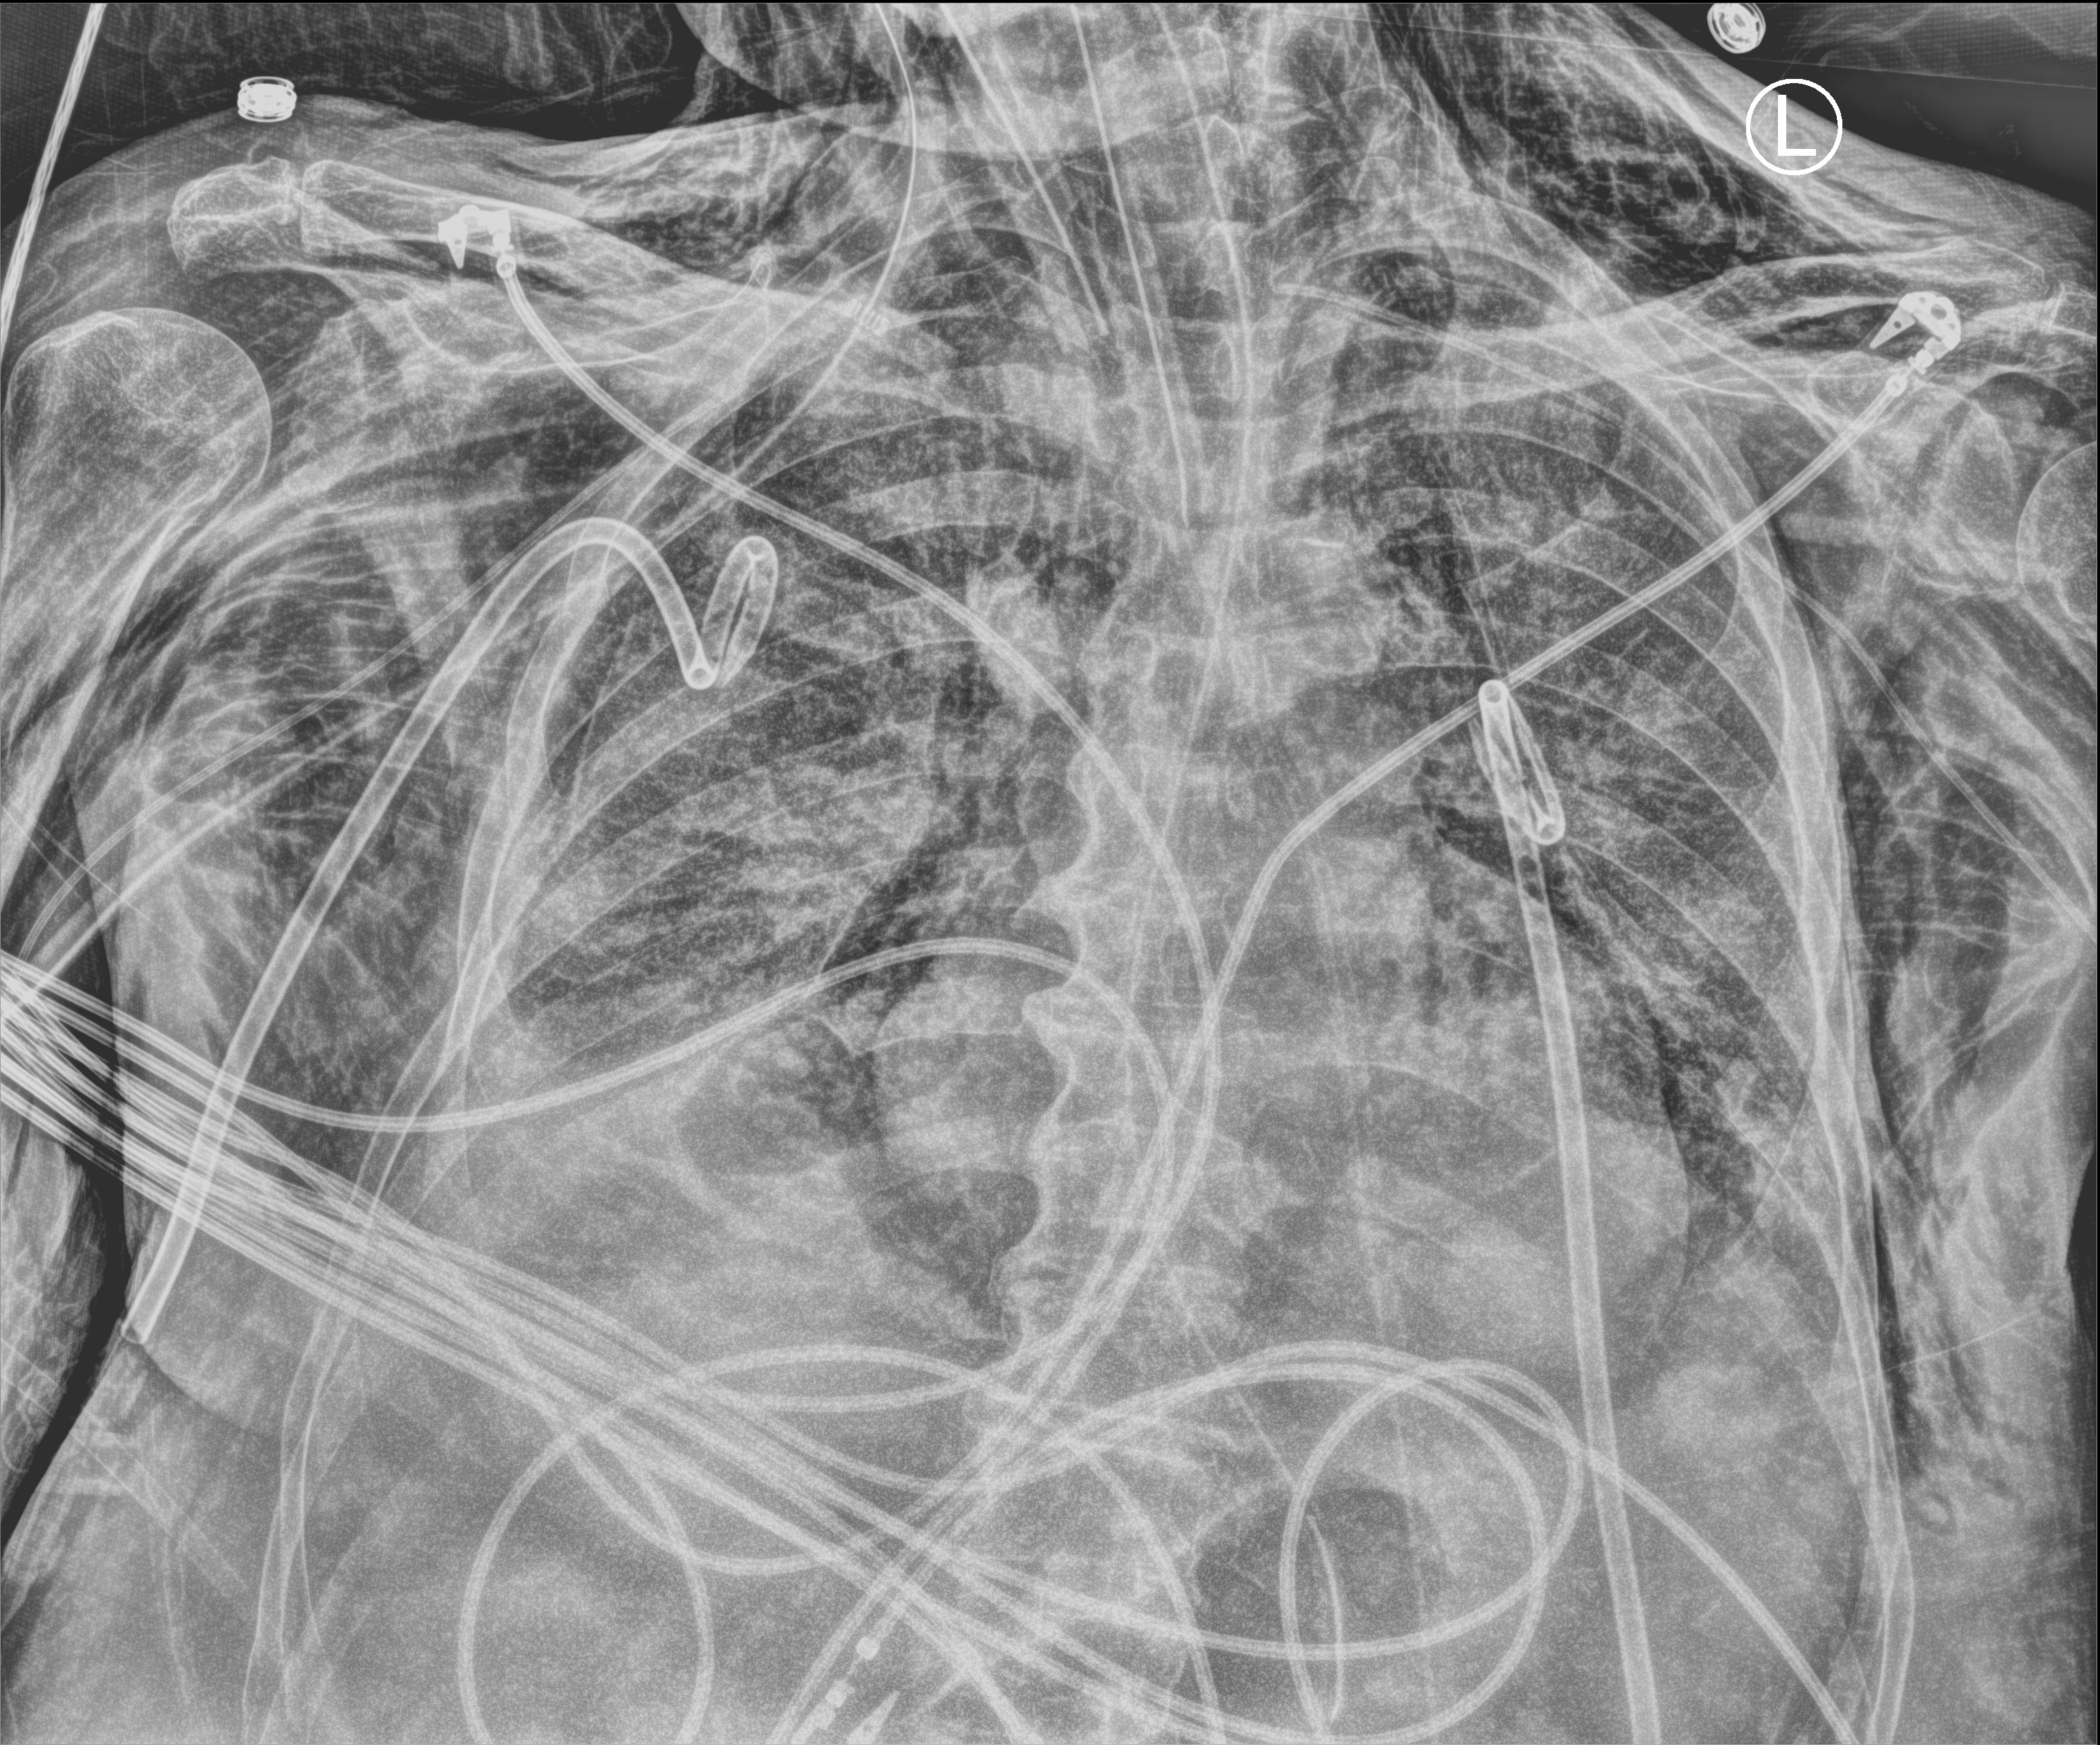
Portable chest radiograph; anteroposterior (AP) projection. Male patient hospitalised with COVID-19, age 75–90 years.
Hospital-stay facts (about this admission, not read from this image; timing relative to this image not recorded): length of hospital stay: 30 days; admitted to intensive care during this hospital stay: yes; mechanically ventilated during this hospital stay: yes.